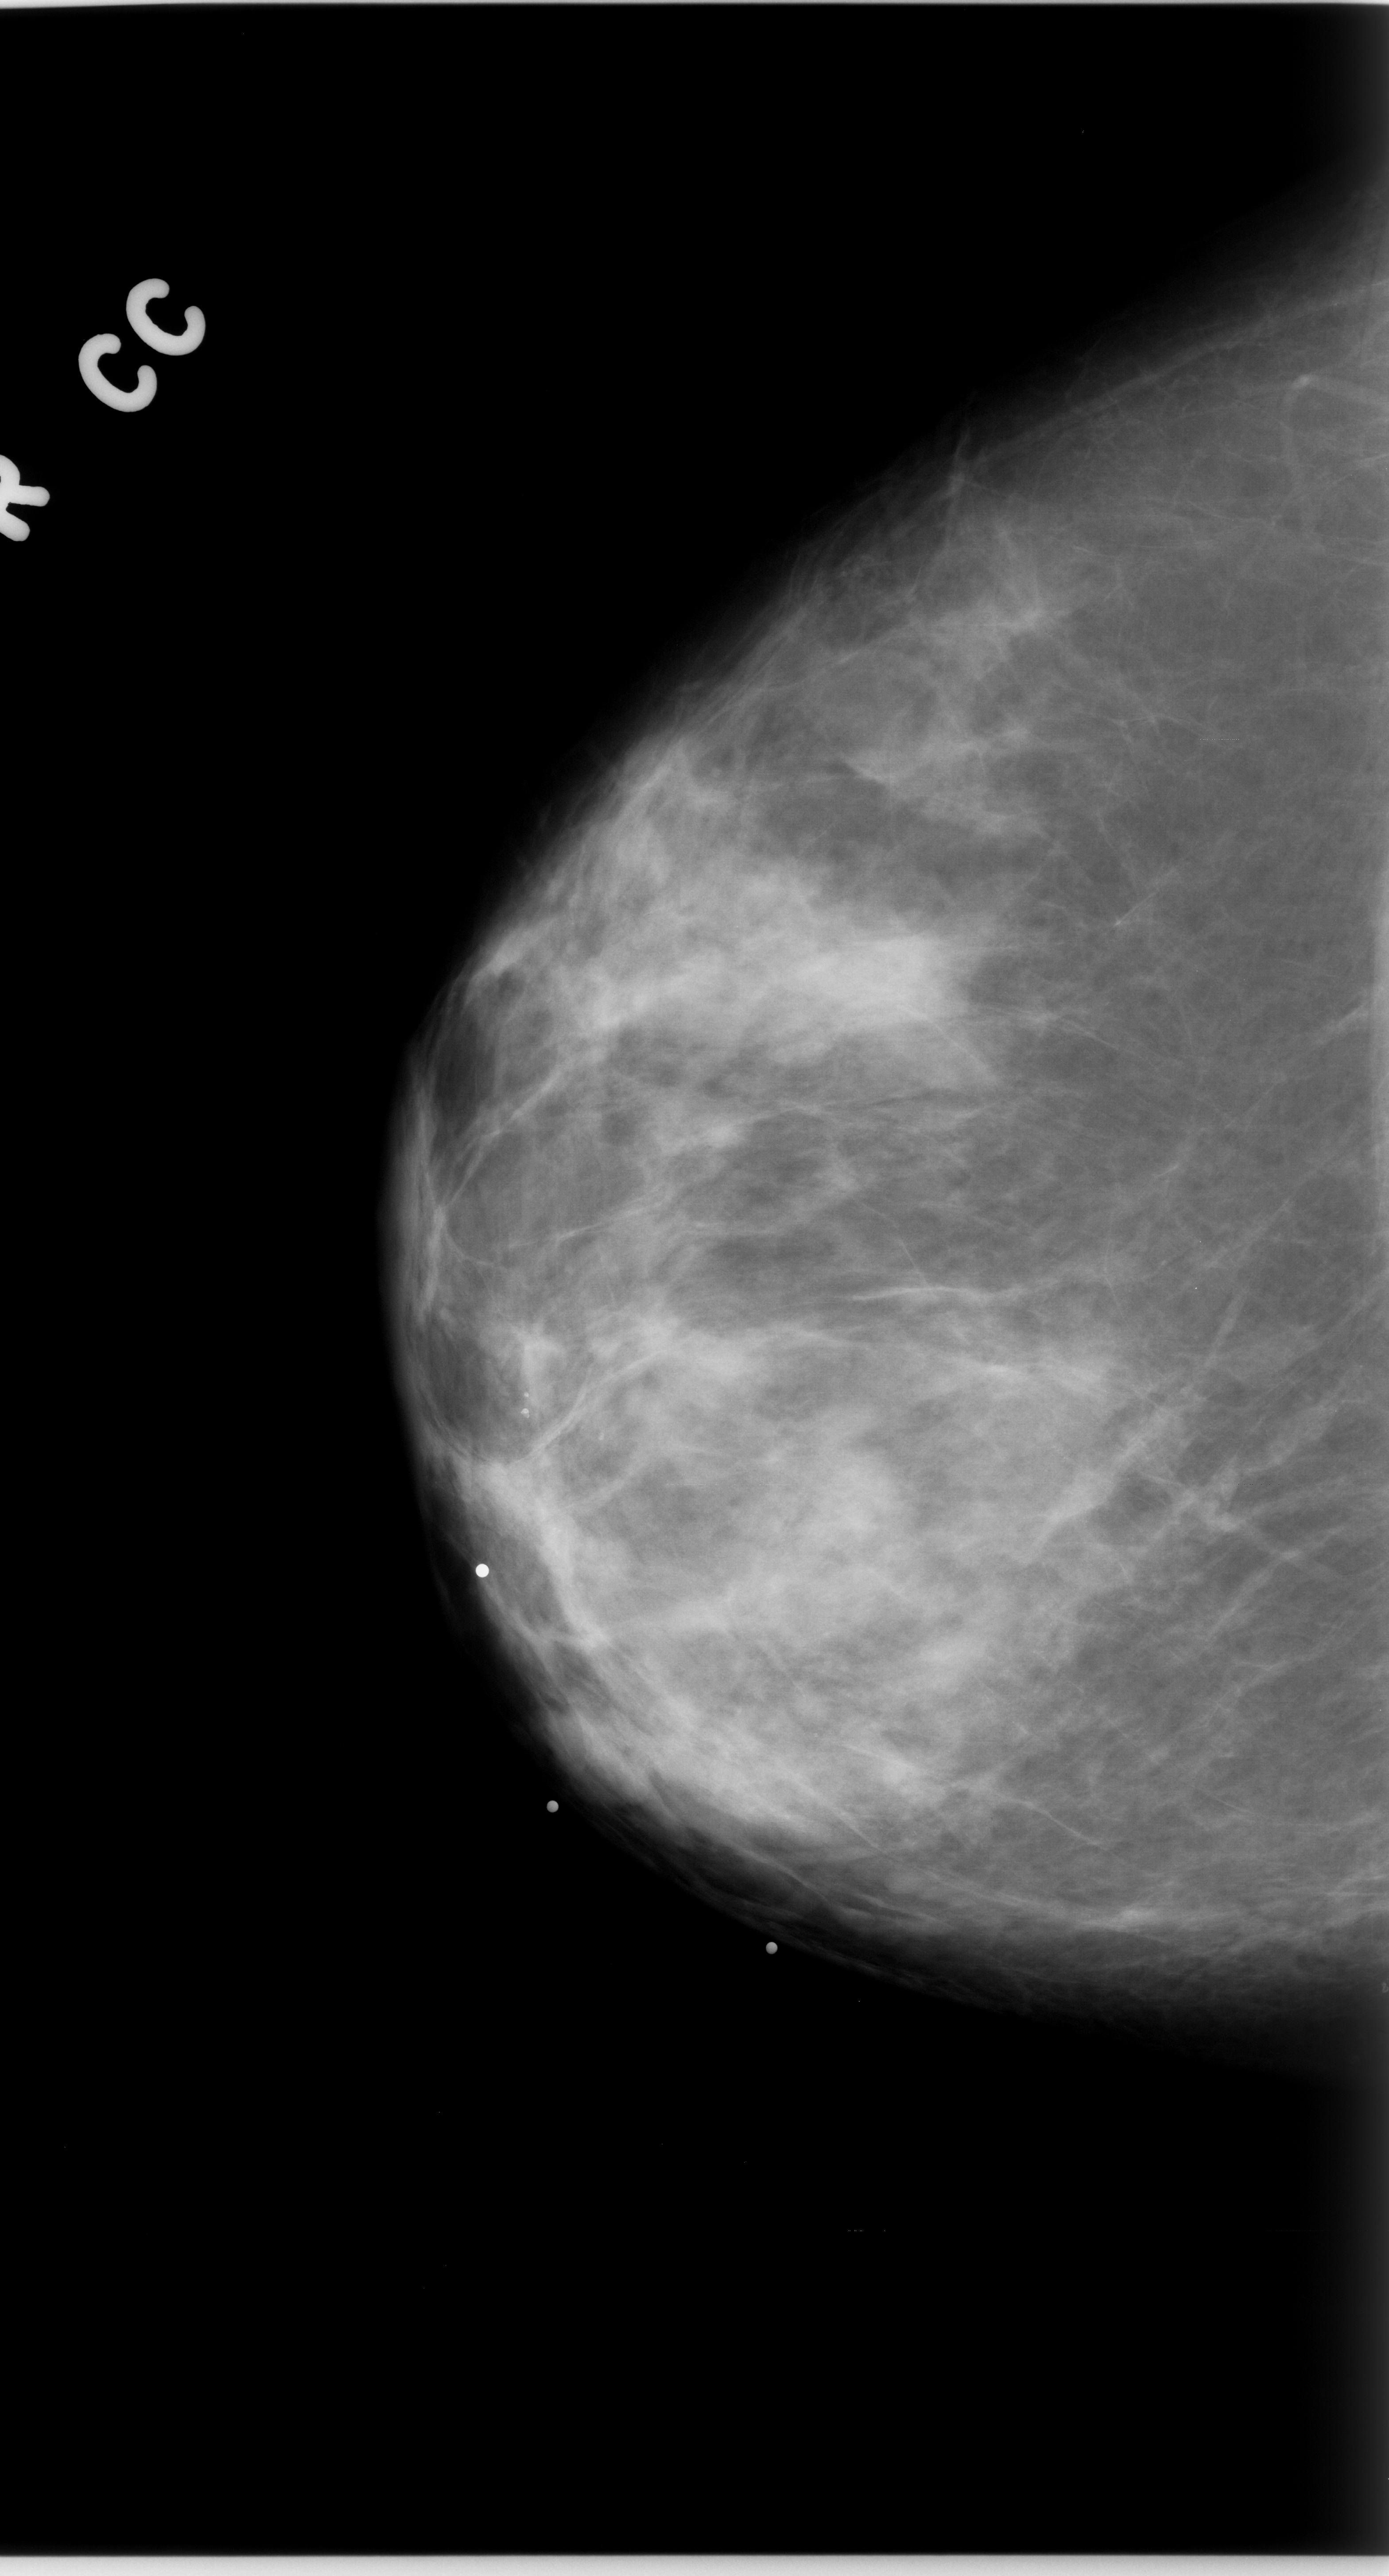
Digitized screen-film mammogram, right breast, craniocaudal (CC) view, BI-RADS breast density category 2 (scale 1–4).
Finding: mass, shape oval, margins obscured; BI-RADS assessment category 4; subtlety rating 2 on a 1 (subtle) to 5 (obvious) scale; pathology (as recorded): malignant.